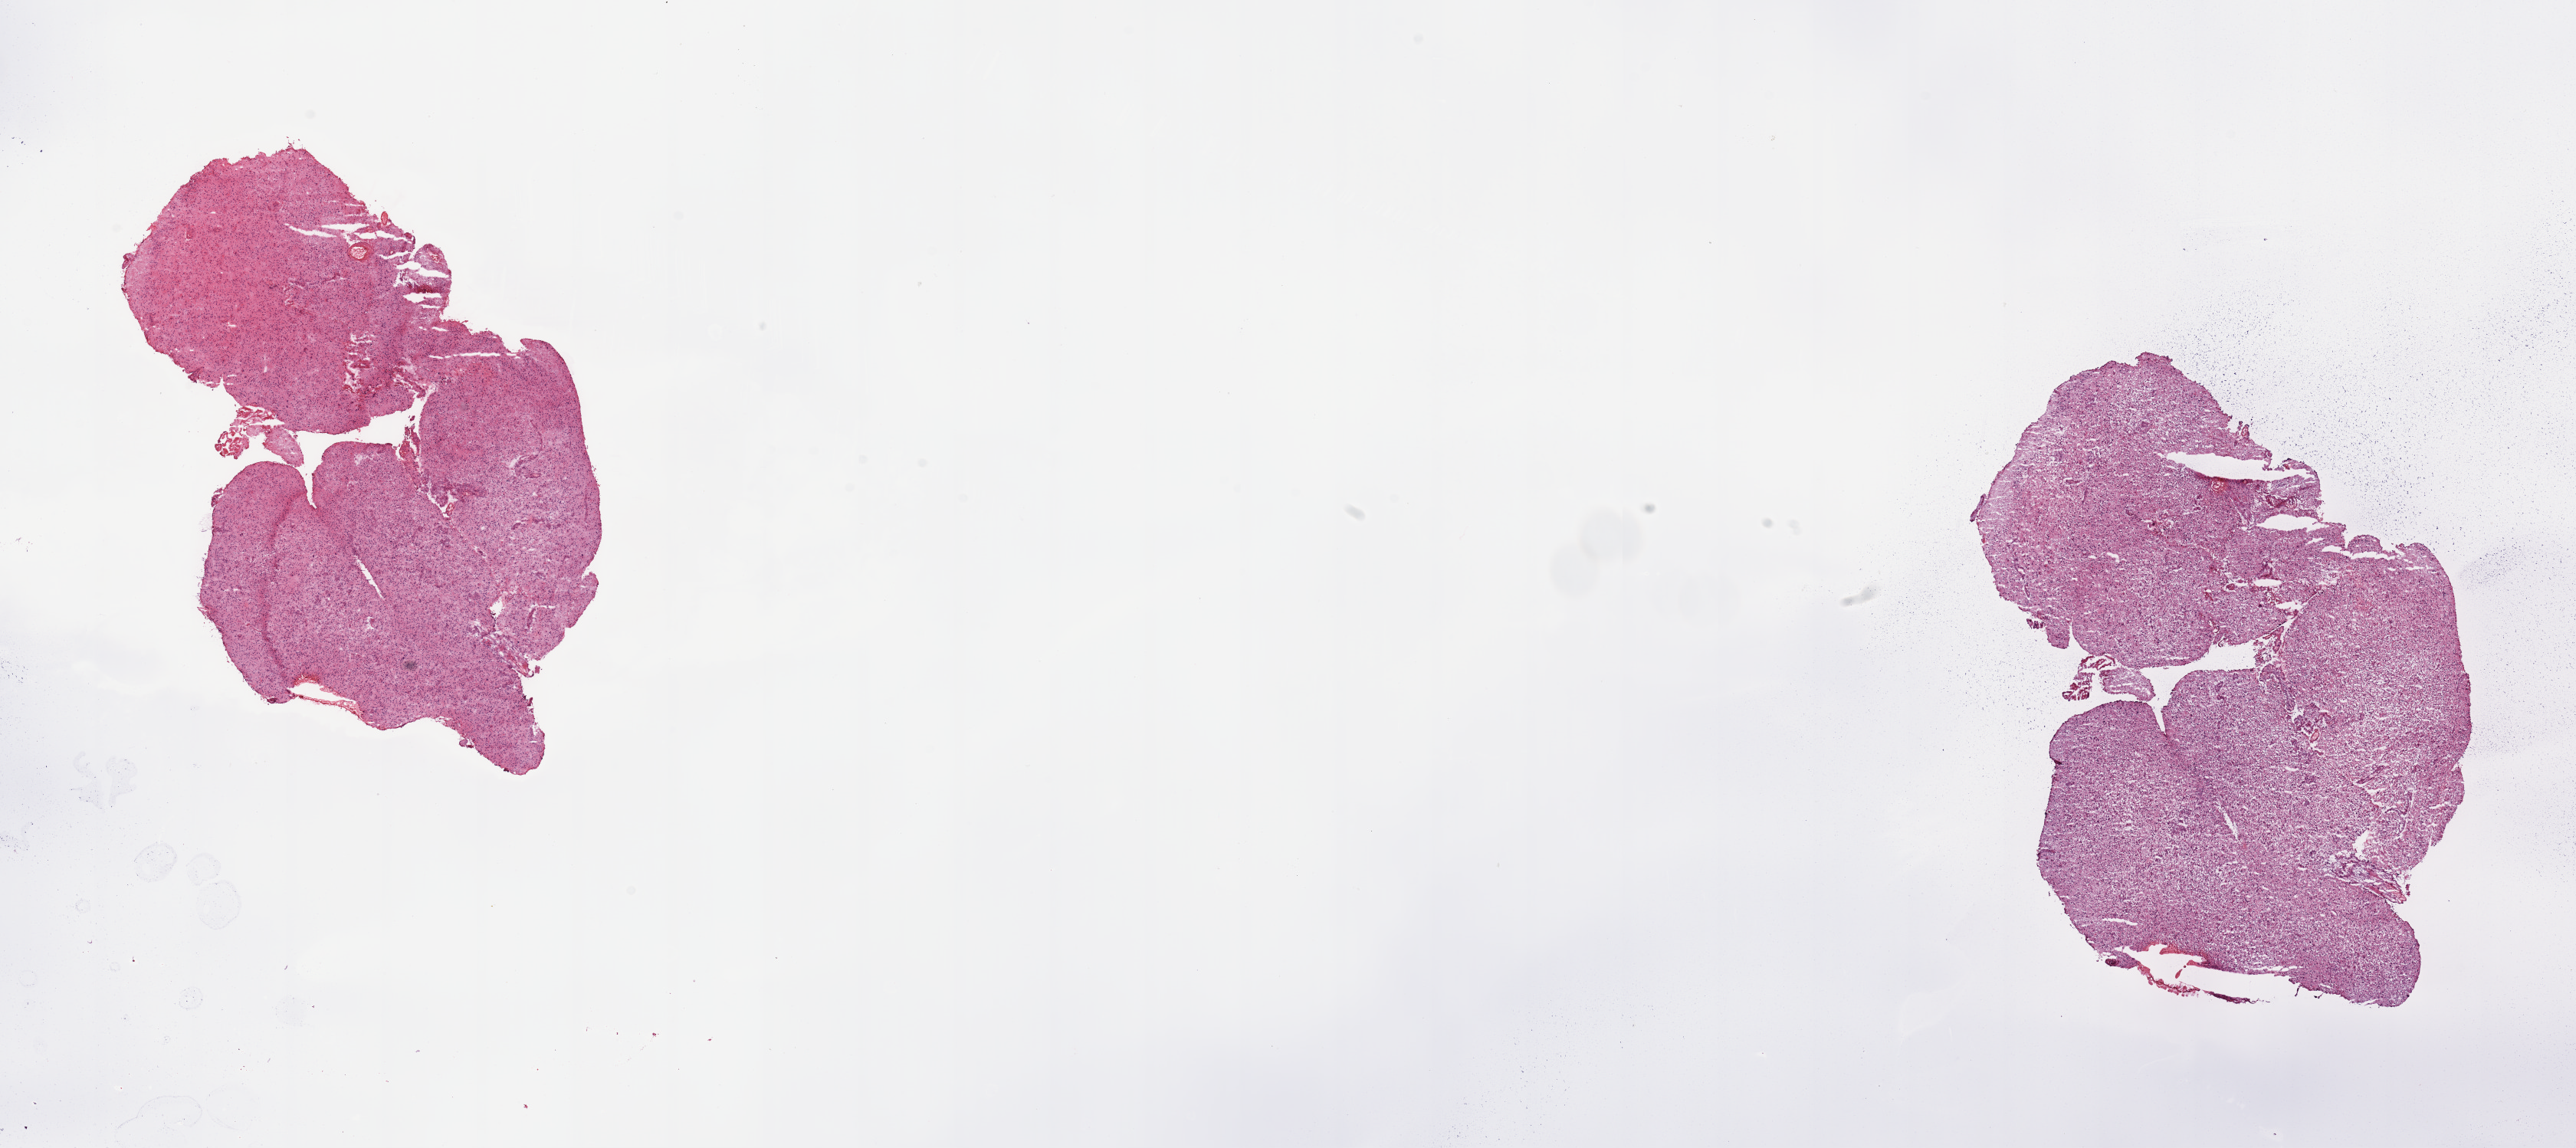
H&E whole-slide image, low-resolution overview of the scanned area, about 26.6 x 11.8 mm; tumour tissue sample, brain. Male, 77 y/o.
Patient diagnosis (cohort enrolment): glioblastoma multiforme (brain).